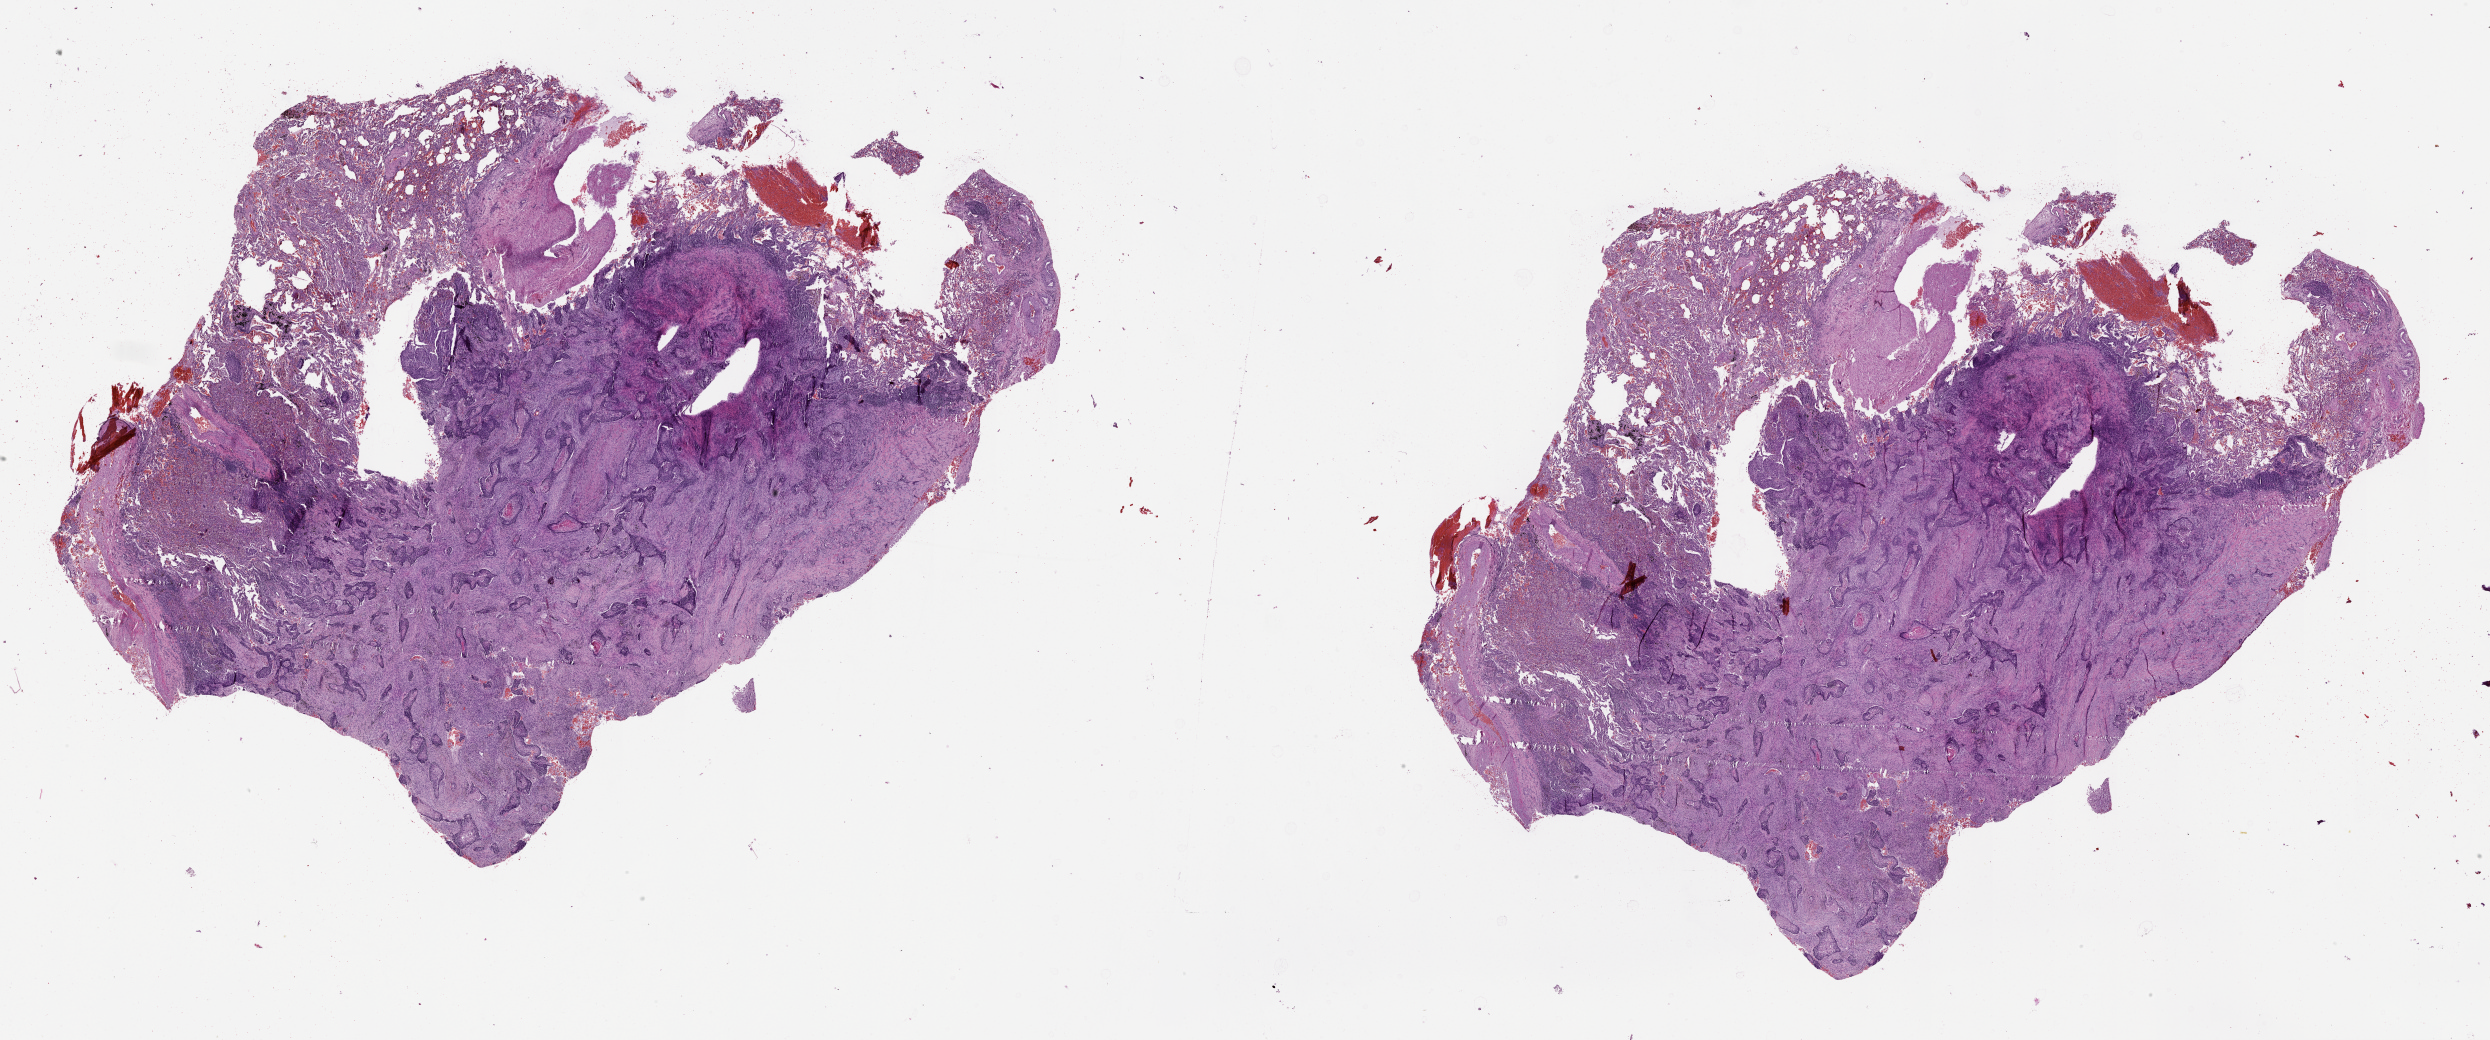
Hematoxylin and eosin (H&E) stained whole-slide image — whole scanned area (about 40.1 x 16.7 mm, from a 20x scan) shown as a low-resolution overview. Tumour tissue sample, lung. 49-year-old male patient.
Patient diagnosis (cohort enrolment): squamous cell carcinoma (lung).